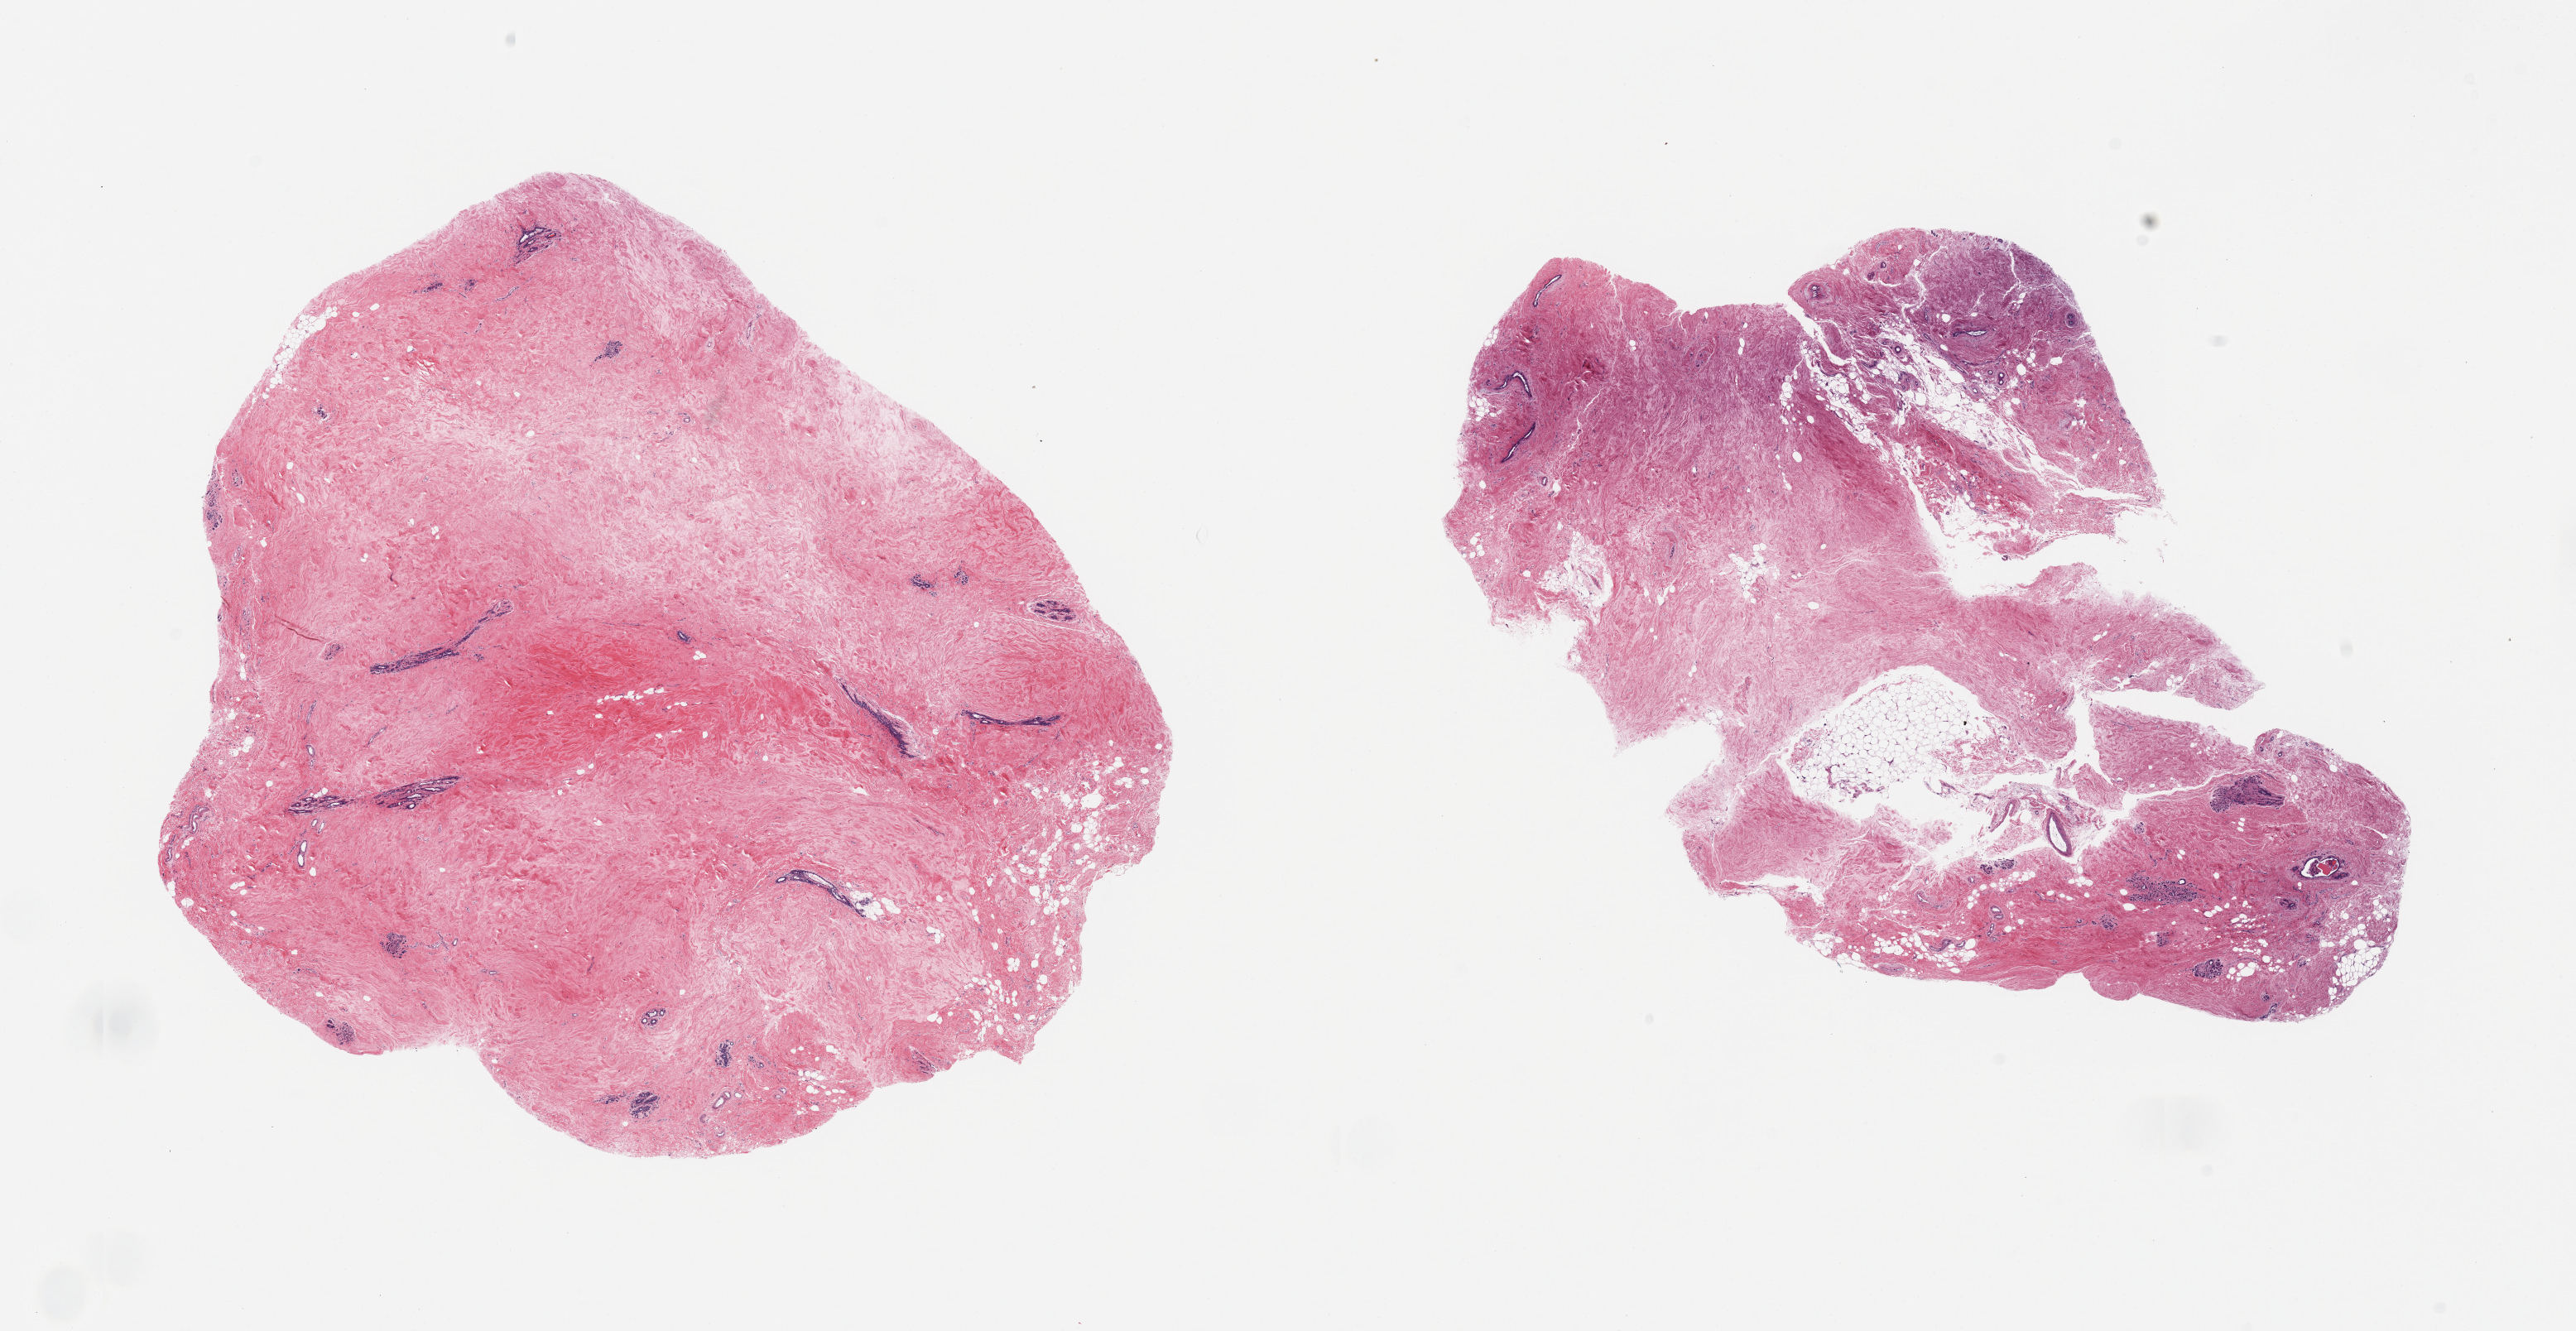
Whole-slide image, H&E stain — low-resolution overview of the scanned area, about 24.6 x 12.7 mm. PAXgene-fixed paraffin-embedded (PFPE) section. Target tissue: breast. Donor tissue sample. Donor: female.
Pathologist's review note for this sample: 2 pieces; atrophic lobules and fibrosis.